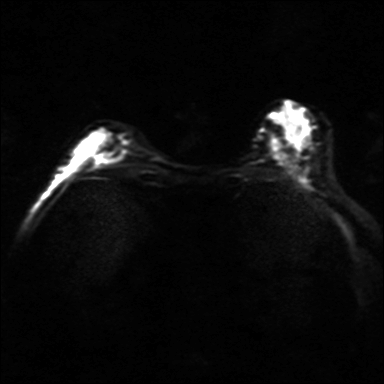
Breast MRI, one axial slice; slice 15 of 36 in the series (ordered by position); diffusion-weighted series; image 2 of 4 stored at this slice position (different b-values; order by instance number); 3 T; 4 mm slice thickness; 384 × 384 image matrix, field of view 320 × 320 mm. Female patient.
Annotated regions visible in this slice (expert manual segmentation):
- tumour on diffusion-weighted imaging: bounding box [x1, y1, x2, y2] px = [99, 133, 133, 161]